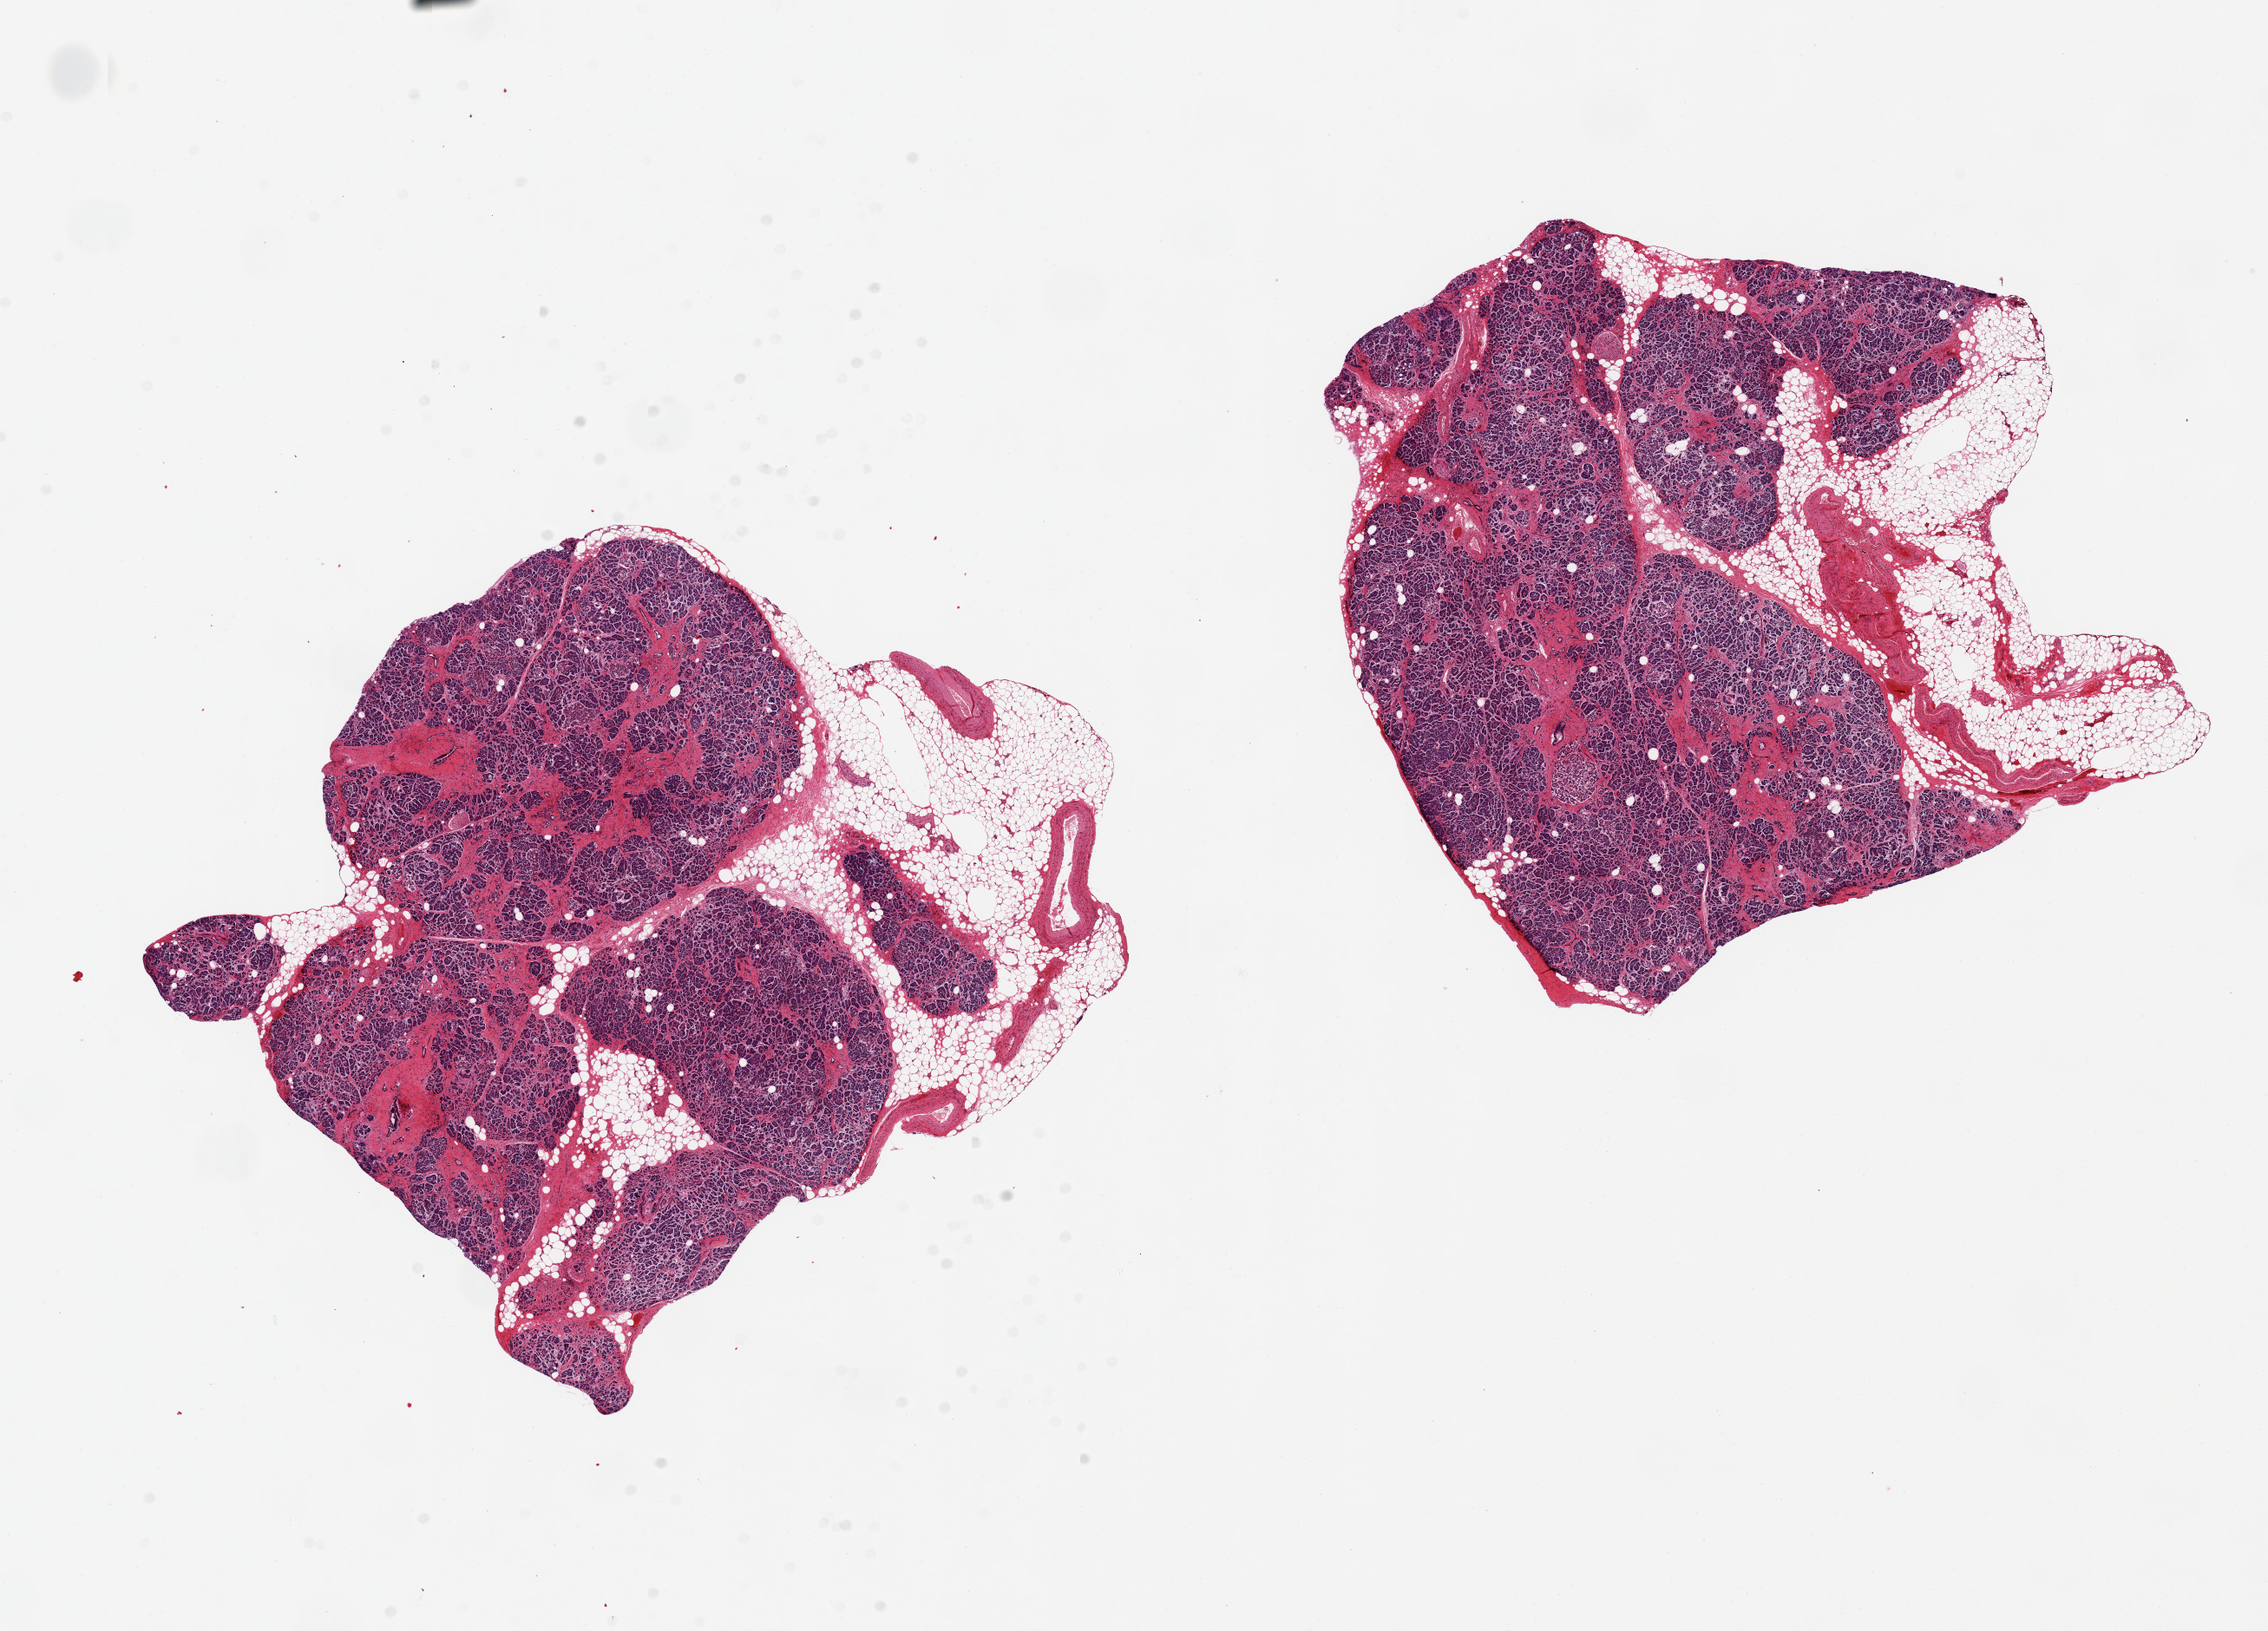
Digitized H&E-stained section, brightfield, low-resolution overview of the scanned area, about 20.7 x 14.9 mm. PAXgene-fixed, paraffin-embedded tissue. Target tissue: pancreas. Donor tissue sample. Donor sex: male.
Reviewer comment on this tissue sample: 2 pieces, 8x6 & 7x6mm; moderate interstitial fibrosis; 25% adipose within and outside.